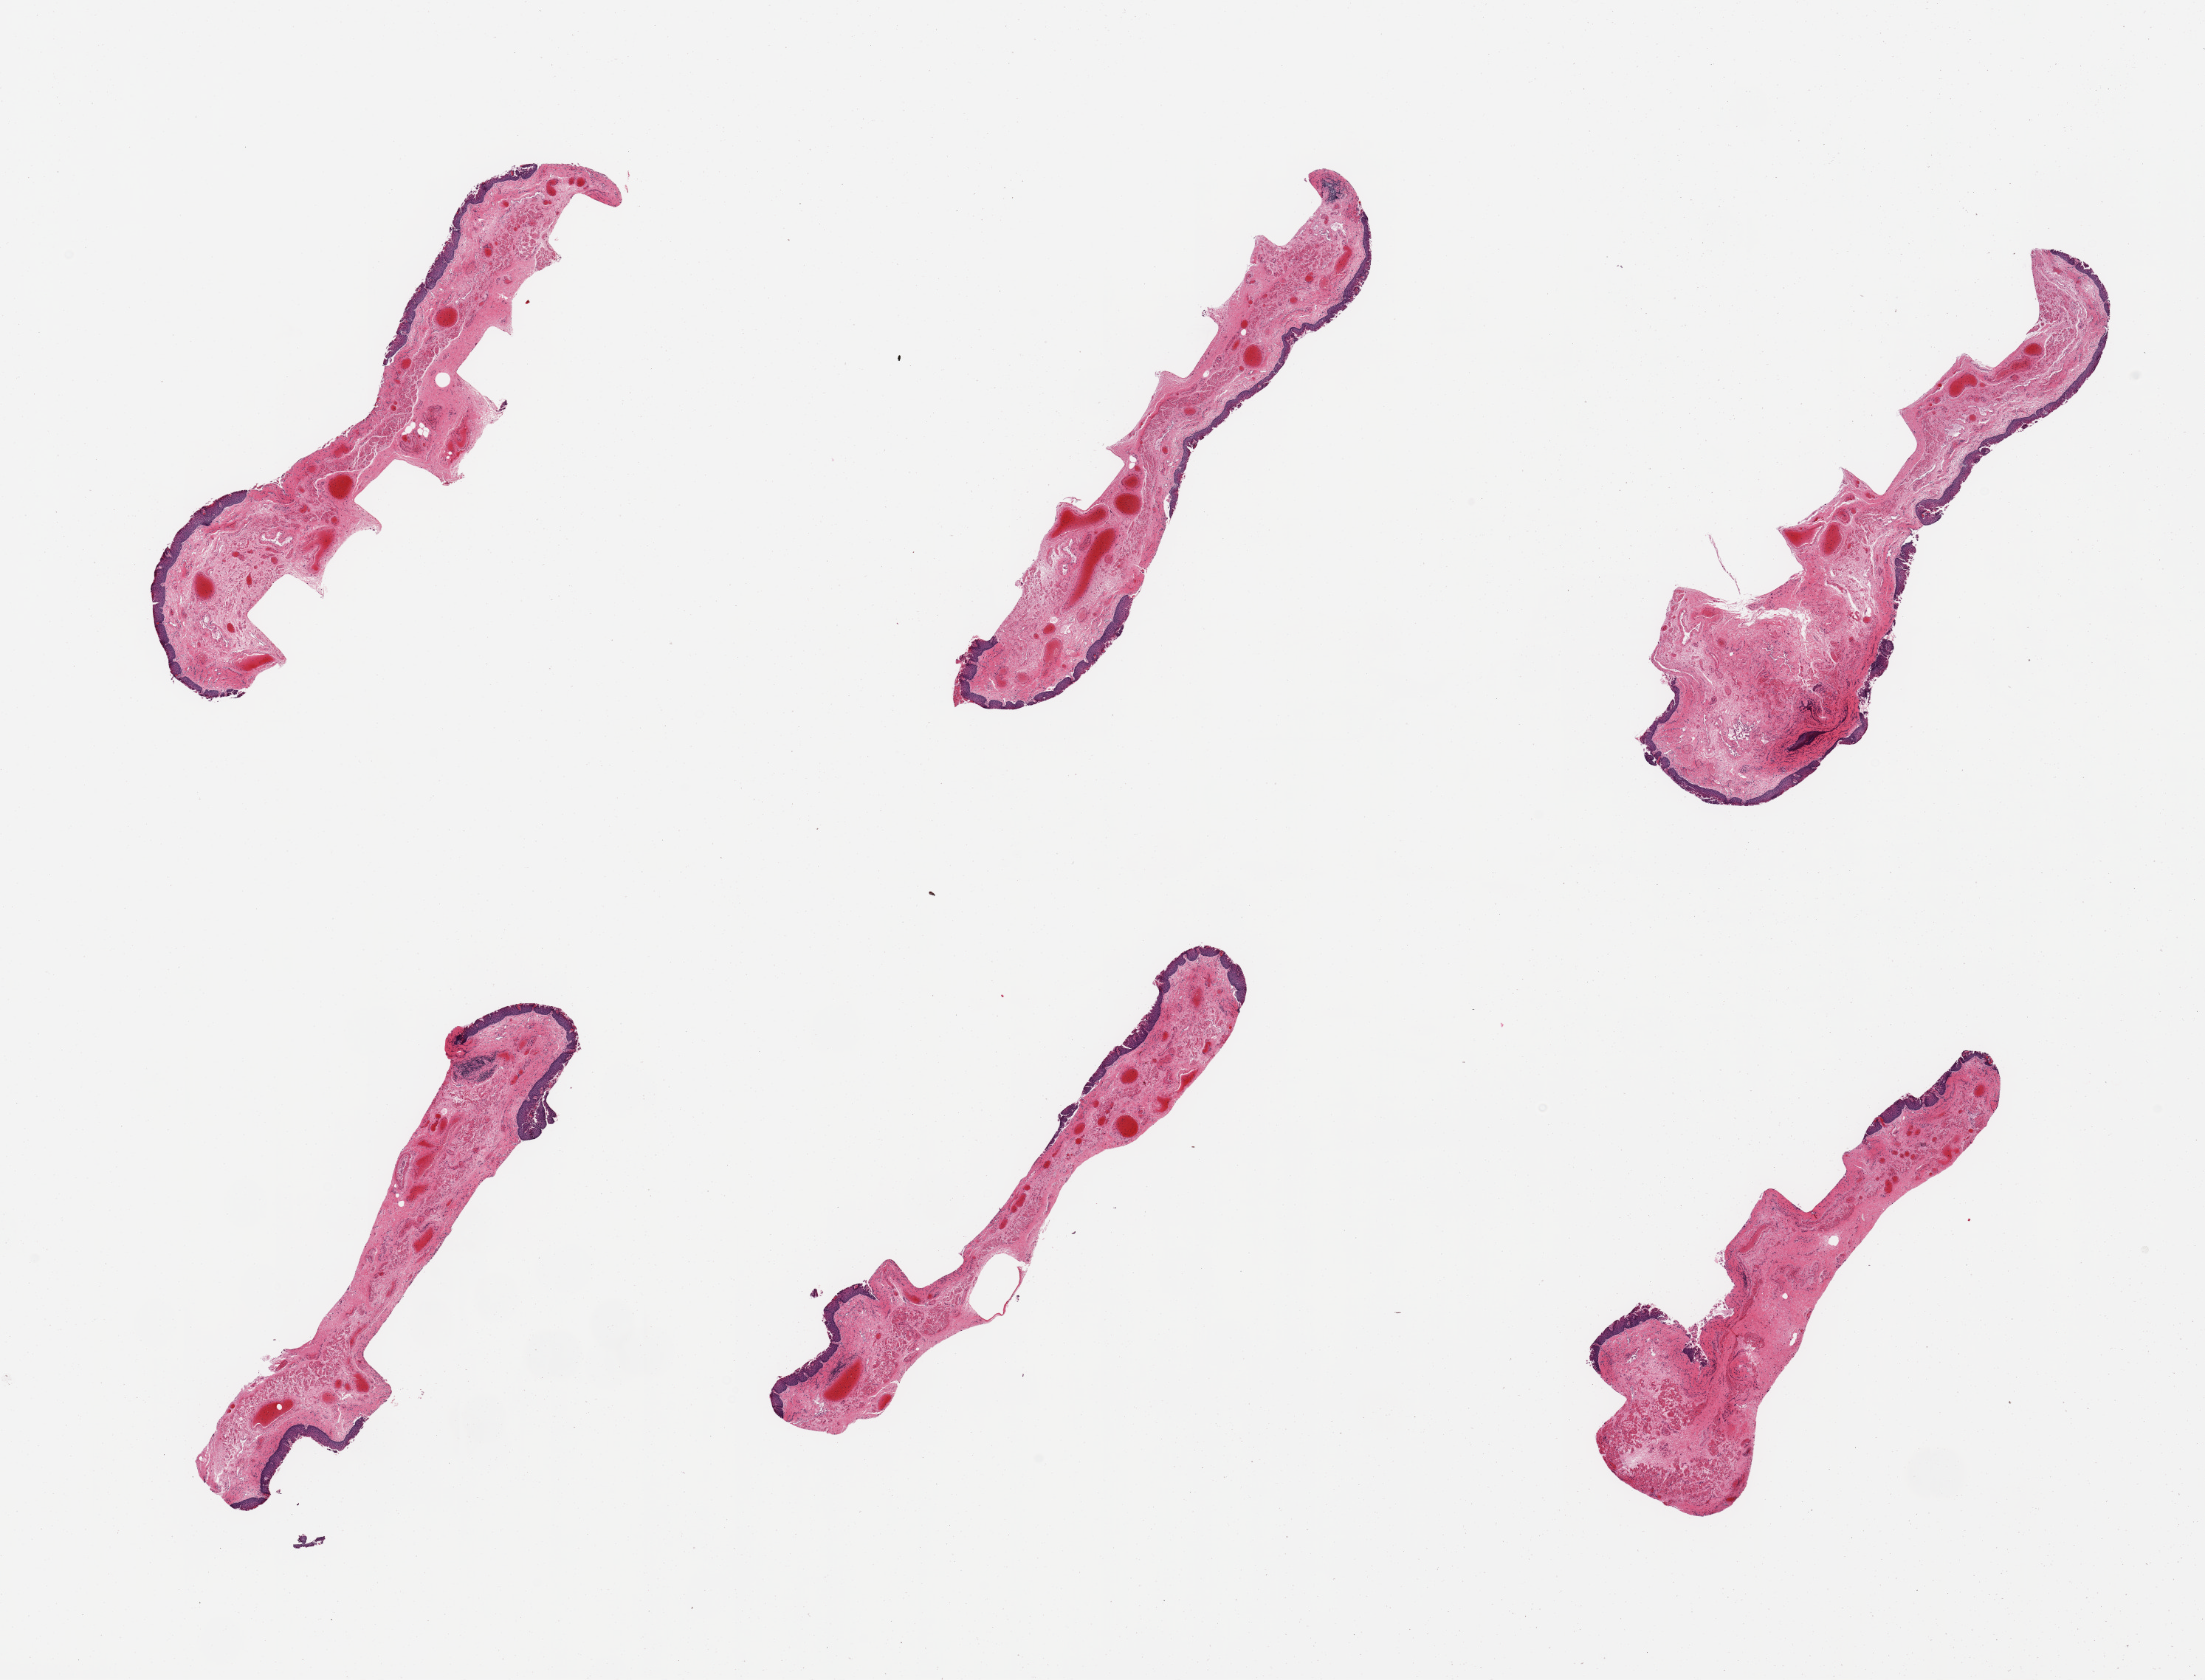
Digitized haematoxylin and eosin-stained section — shown as a low-resolution overview of the whole scanned area (about 23.6 x 18.0 mm). PAXgene-fixed paraffin-embedded (PFPE) section. Target tissue: esophageal mucous membrane. Tissue donor sample. Donor sex: female.
- reviewer comment on this tissue sample: 6 pieces, squamous mucosa sloughing, residual up to ~0.1mm